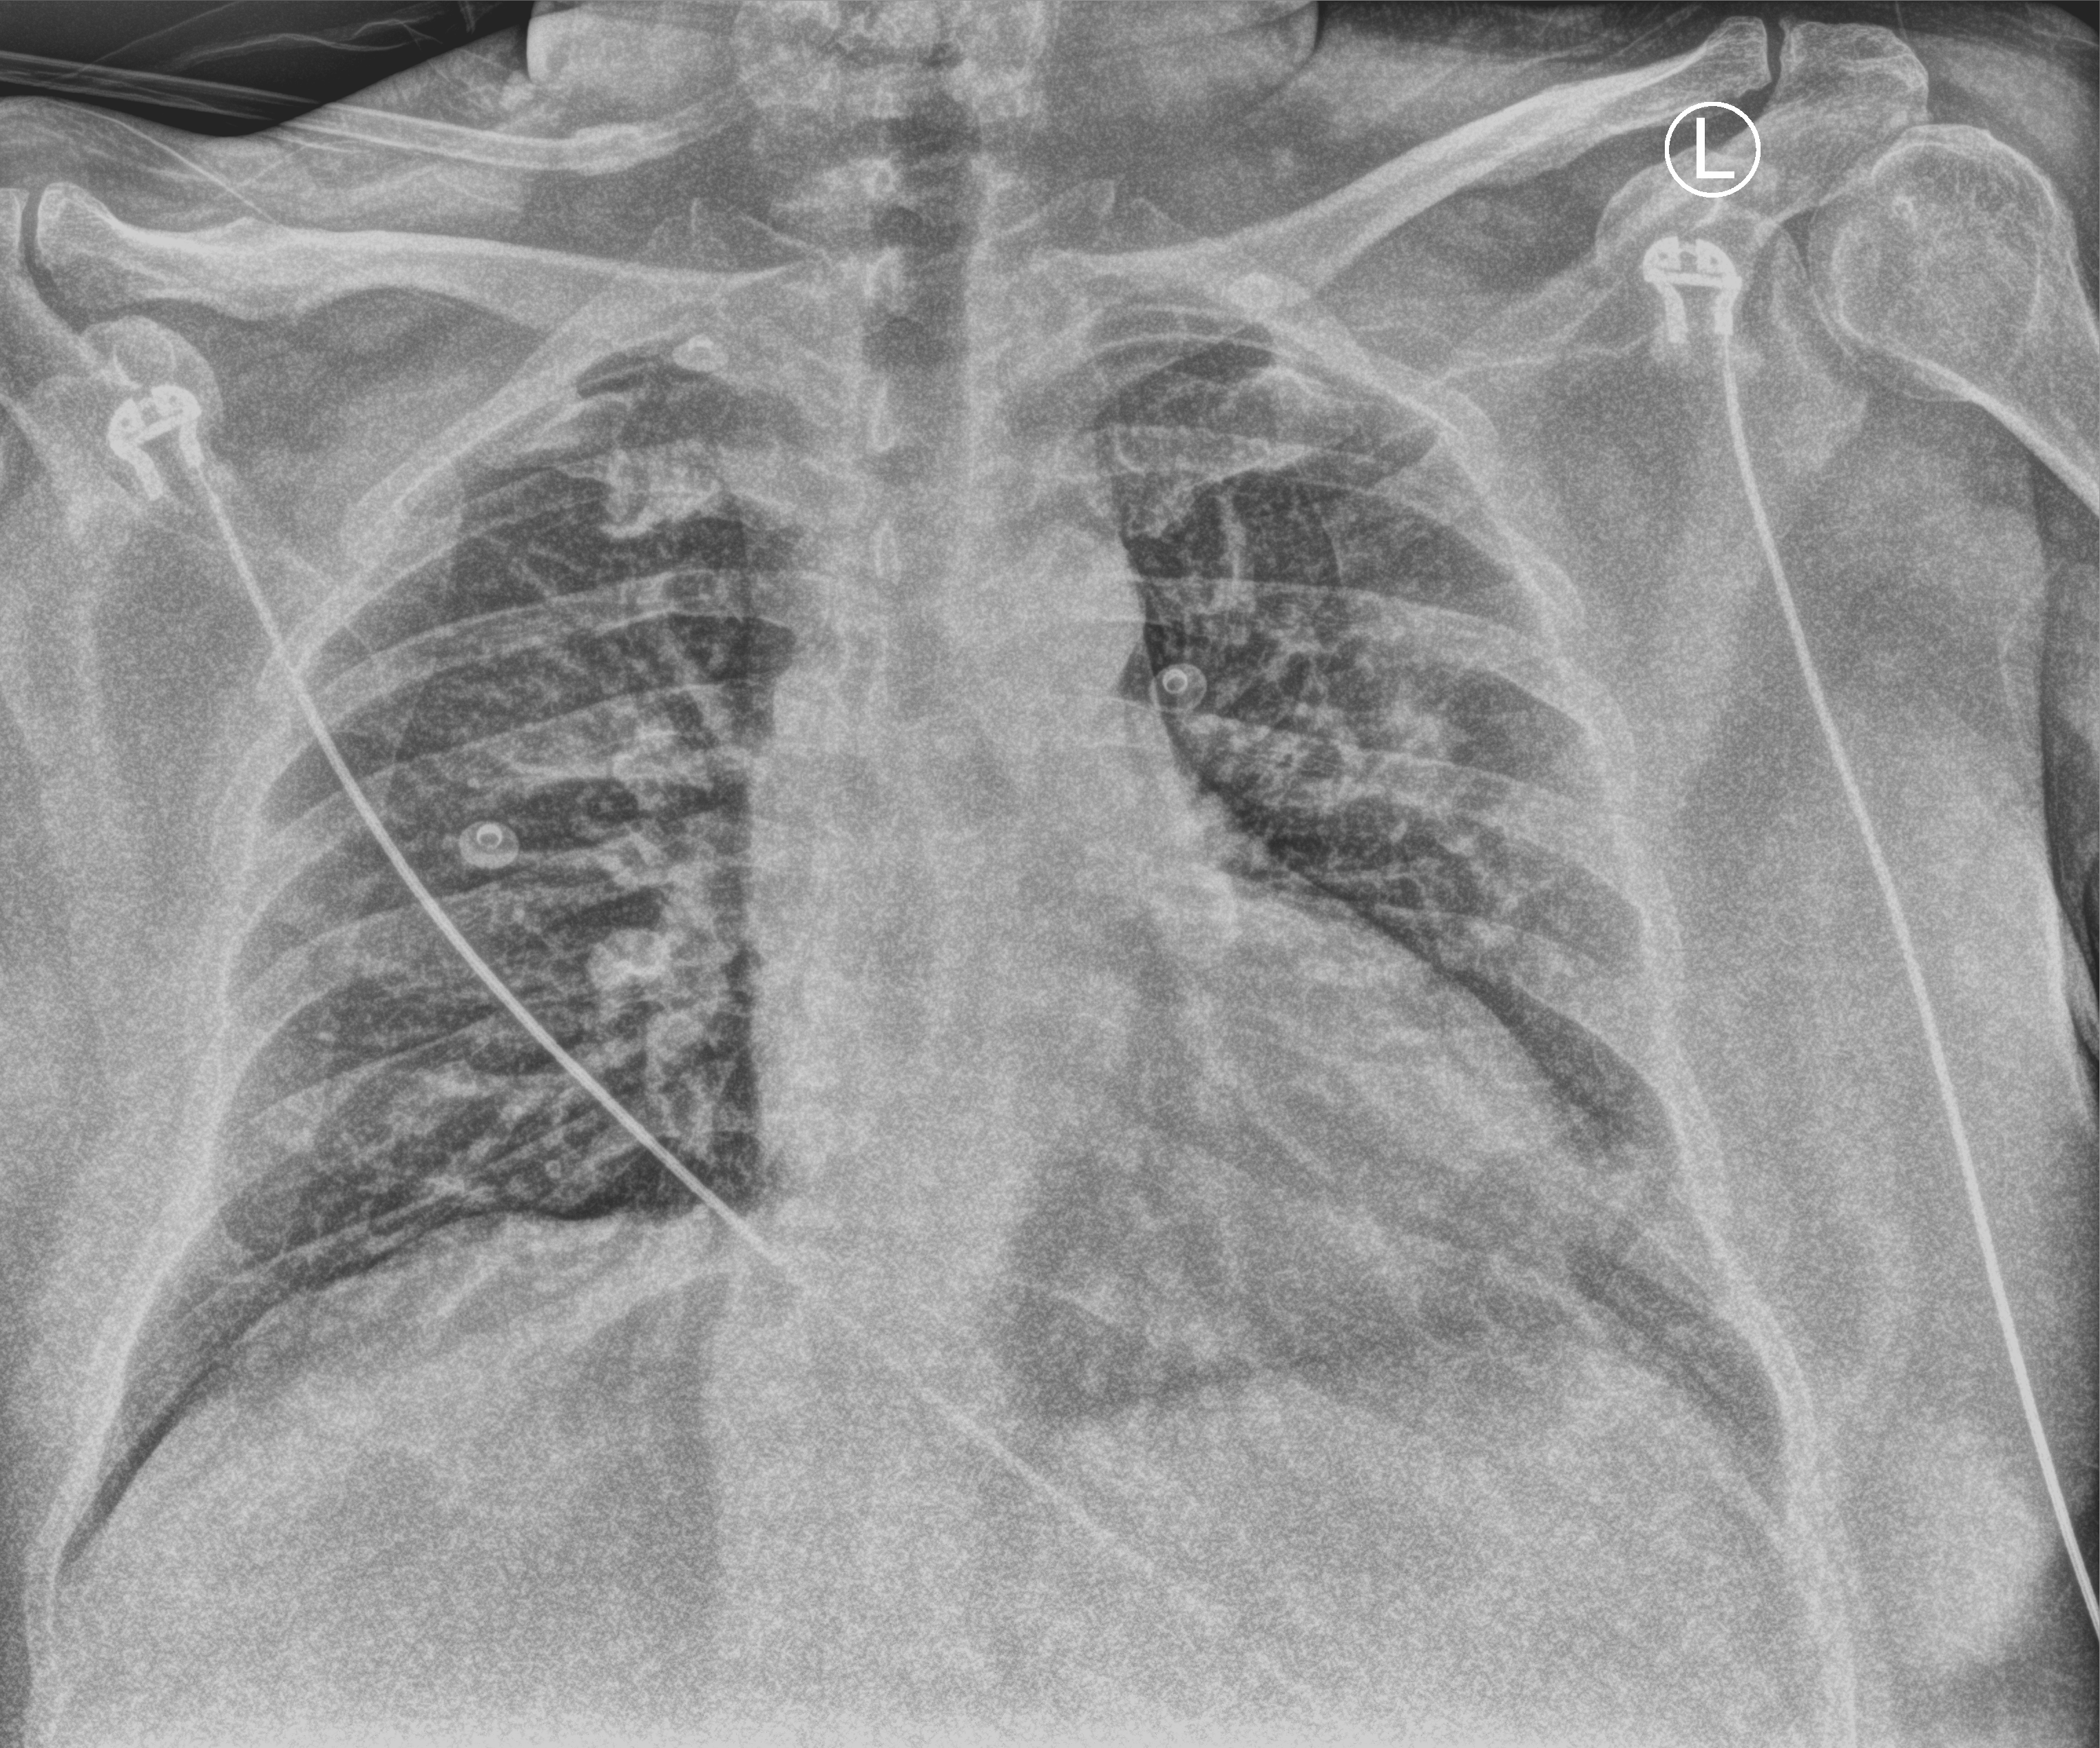
Portable chest radiograph, anteroposterior (AP) projection. Patient hospitalised with COVID-19; male, aged 18–59 years.
Hospital-stay facts (about this admission, not read from this image; timing relative to this image not recorded): hypertension (admission record): yes; diabetes (admission record): yes.